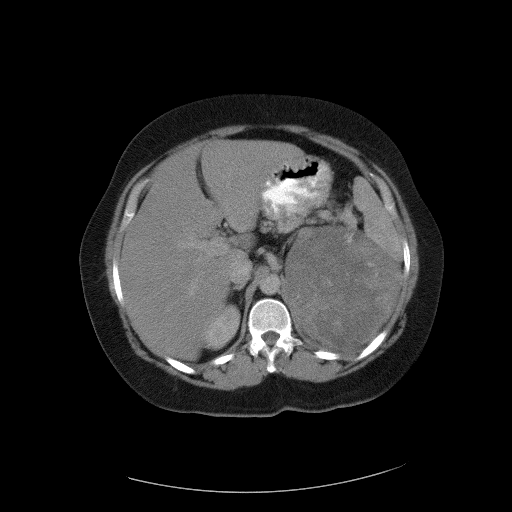
Contrast-enhanced abdominal CT, one axial slice. Slice 71 of 90 in the series (ordered by position). Intravenous contrast given. Soft-tissue window (W 400 / L 40 HU). 5 mm slice thickness. 512 × 512 image matrix, field of view 480 × 480 mm. Female patient, age 55 years. From the clinical record (not read from this slice): diagnosis: adrenocortical carcinoma; tumour side: left adrenal; tumour size at pathology: 22 cm; Ki-67 index: 10 %; stage (as recorded): 3.
Annotated regions visible in this slice (semi-automatic segmentation, software-assisted and operator-edited):
- mass: bounding box <288,228,397,346> (left, top, right, bottom; pixels)